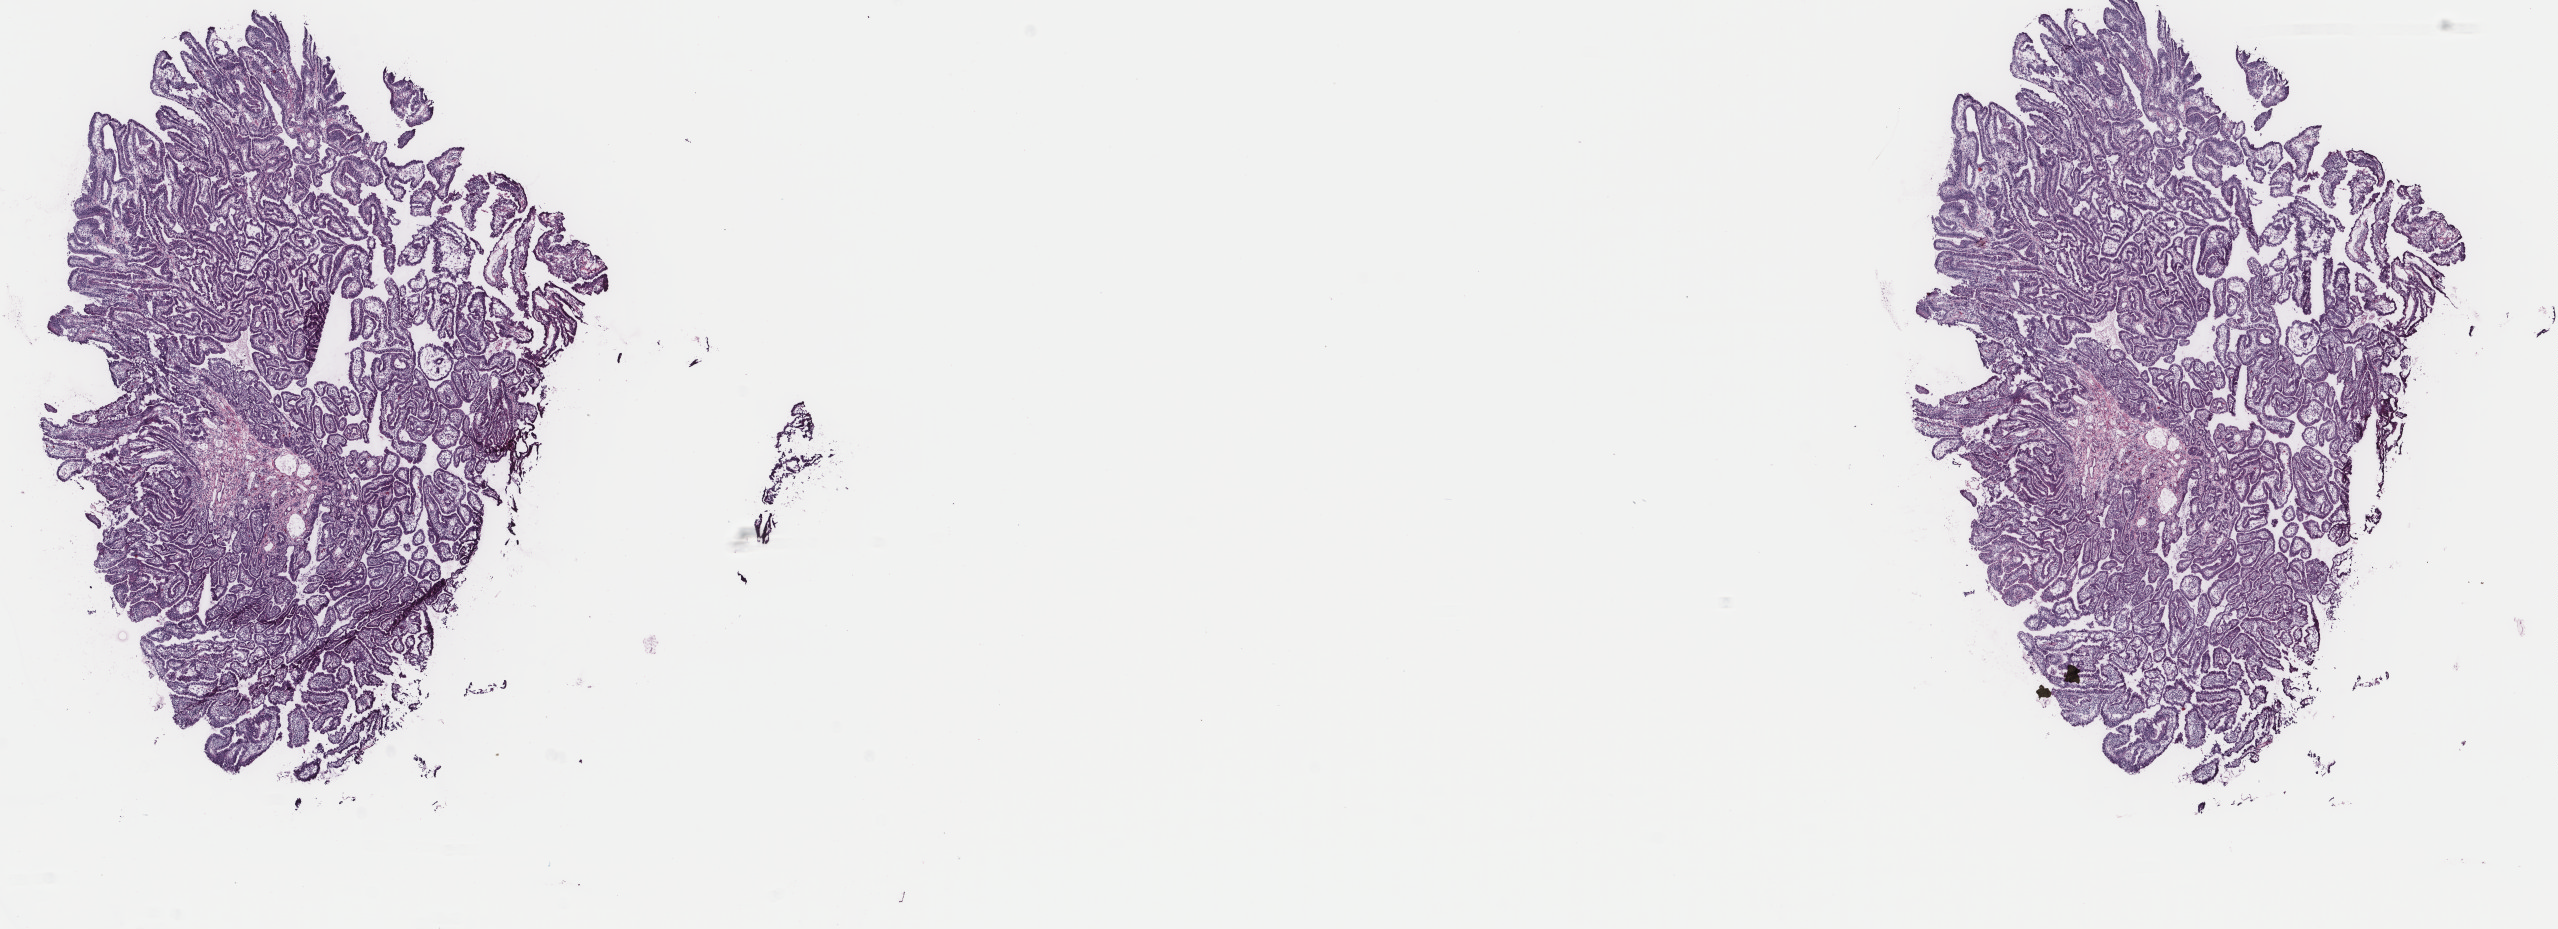
Hematoxylin and eosin (H&E) stained whole-slide image — a low-resolution overview of the entire scanned area, about 20.3 x 7.4 mm. Frozen section from the top of the tissue portion. Primary tumour sample from the esophagus. Male patient; age at initial diagnosis 77 years. Histologic grade: GX (grade cannot be assessed). Pathologist review of this section (percent, as recorded): tumour cells 80%, tumour nuclei 90%, normal cells 0%, stromal cells 20%, necrosis 0%. Infiltration values recorded for this section: lymphocyte infiltration 6%, monocyte infiltration 6%, neutrophil infiltration 0%.
Lymph nodes positive (case pathology): 2 of 10 examined. TNM: T3 N1 MX. AJCC pathologic stage: IIIA (7th edition). Diagnosis: Adenocarcinoma, NOS.